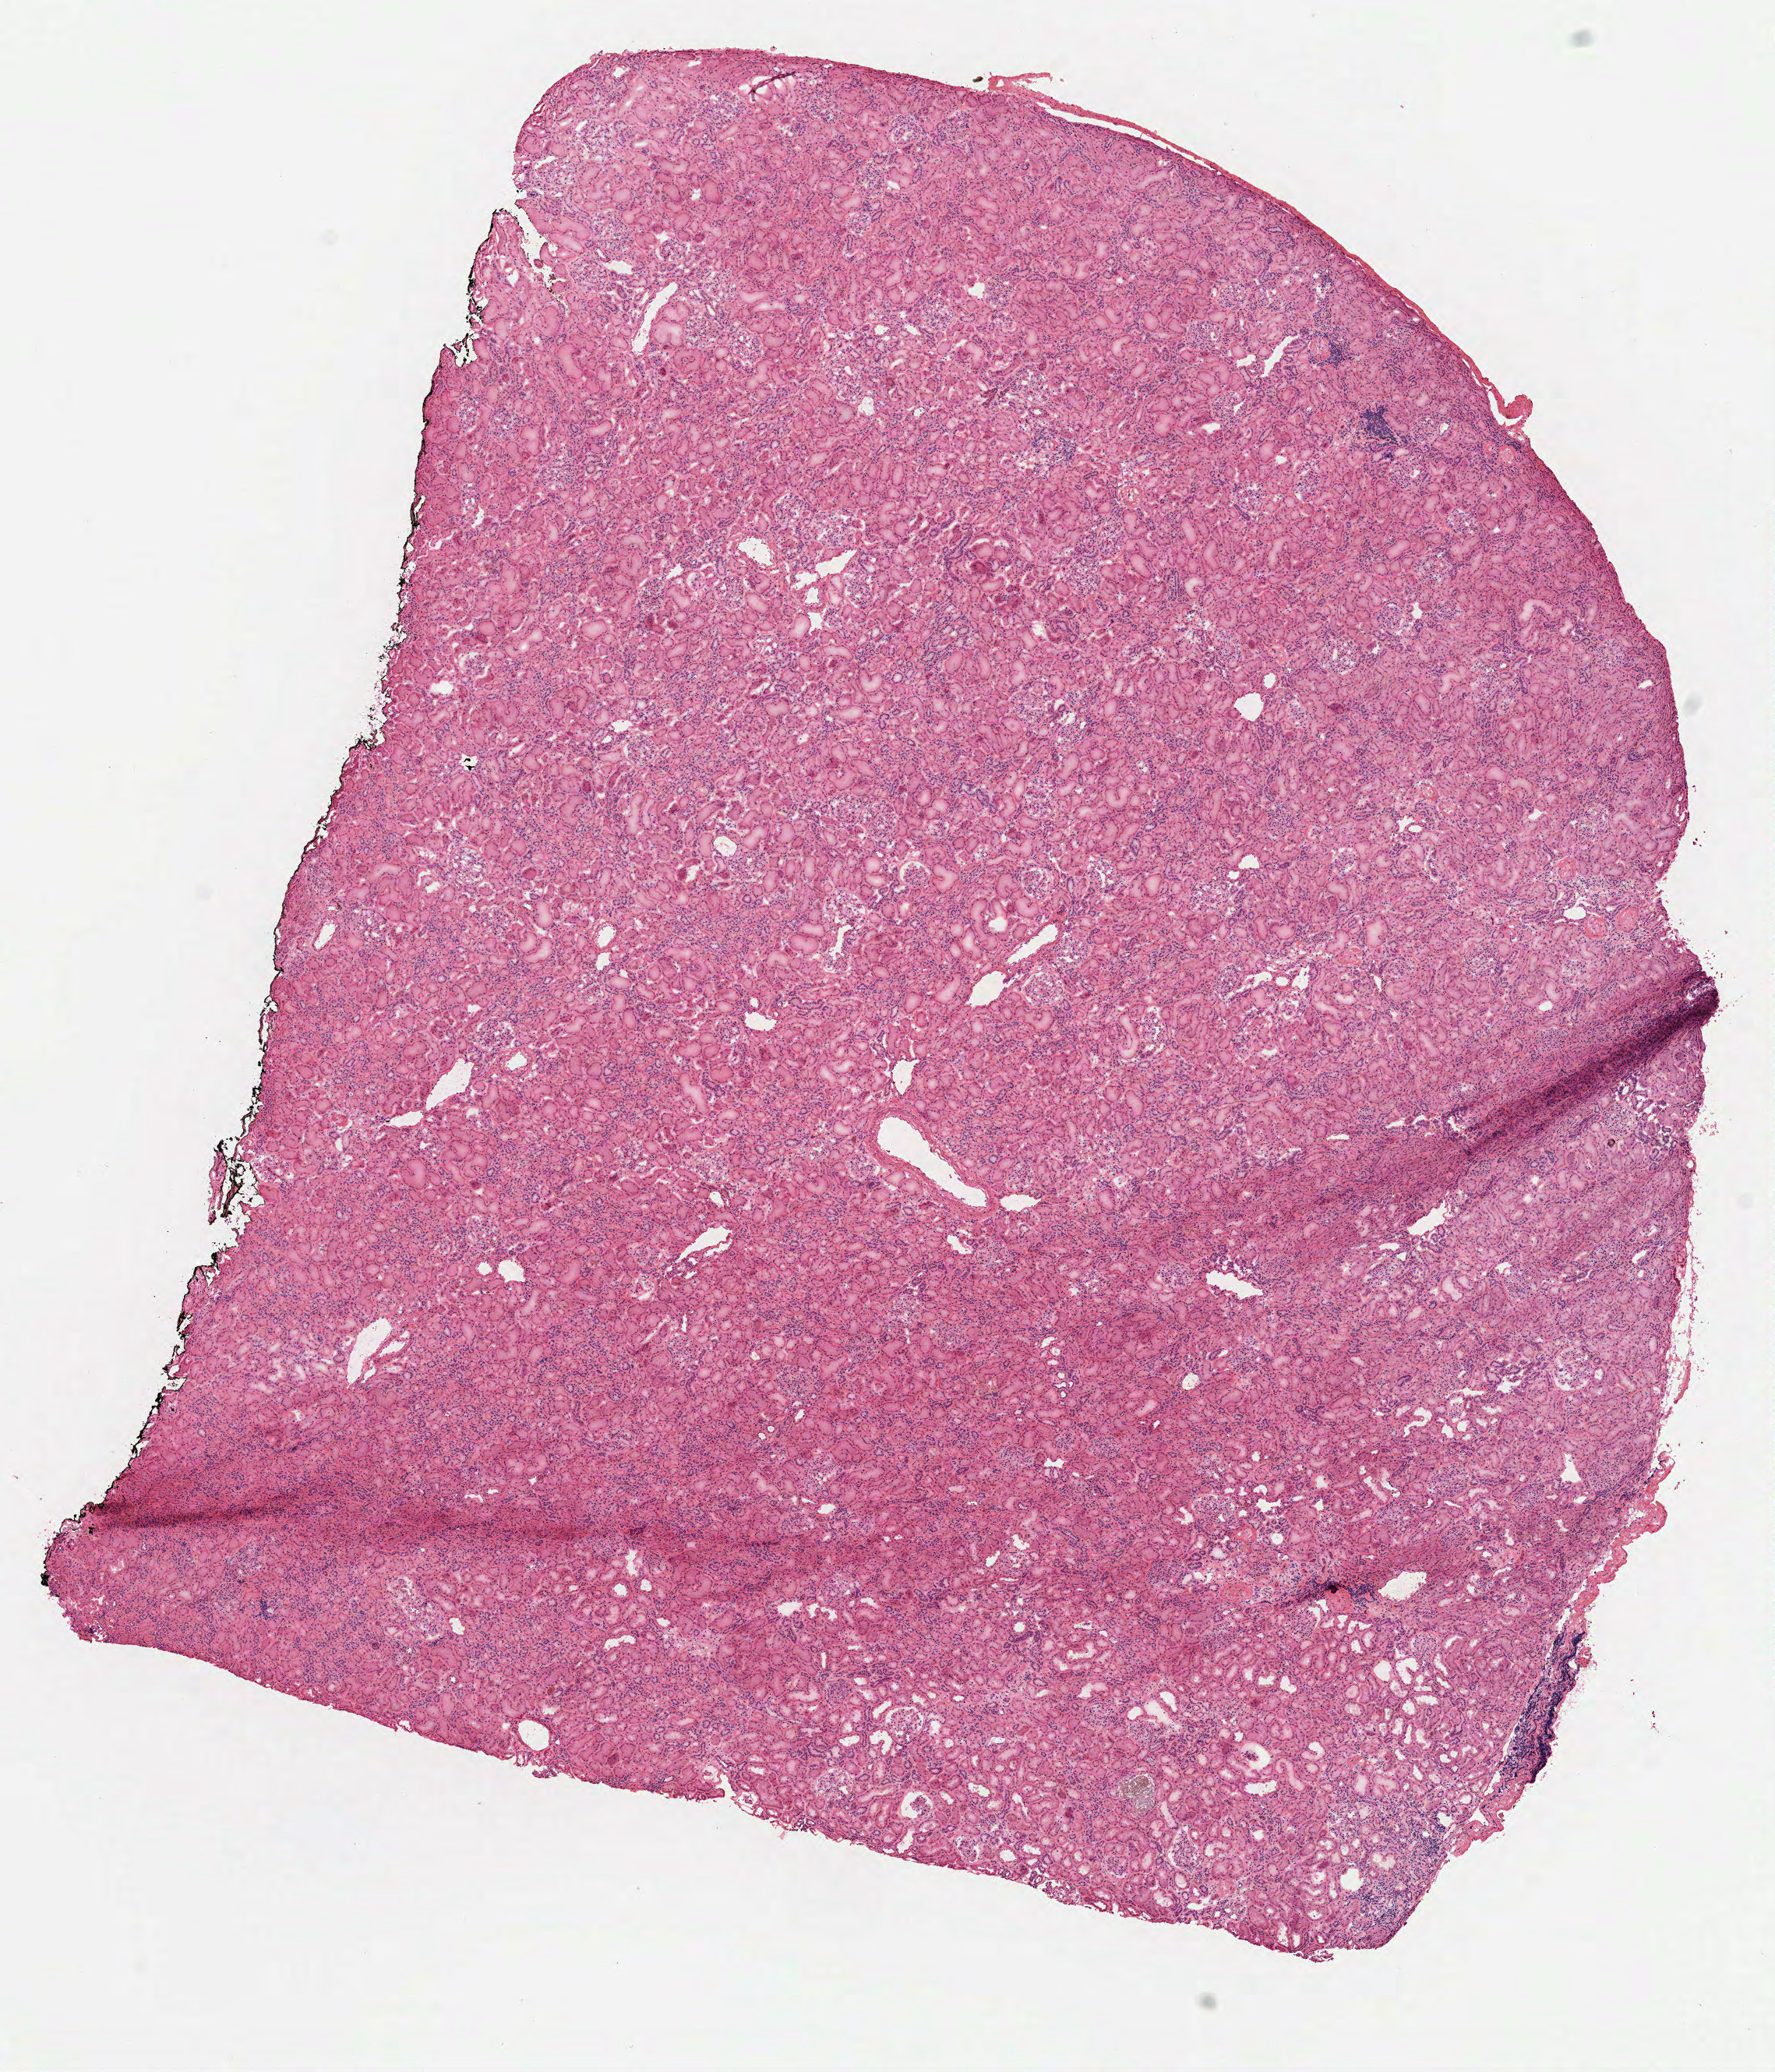
Hematoxylin and eosin (H&E) stained whole-slide image — whole scanned area (about 9.2 x 10.7 mm, from a 40x scan) shown as a low-resolution overview; frozen section from the top of the tissue portion; kidney, solid tissue normal (non-tumour tissue) sample. Patient: female, age at initial diagnosis 53 years.
This section: solid tissue normal (non-tumour) sample from the same patient. Patient diagnosis: Papillary adenocarcinoma, NOS.